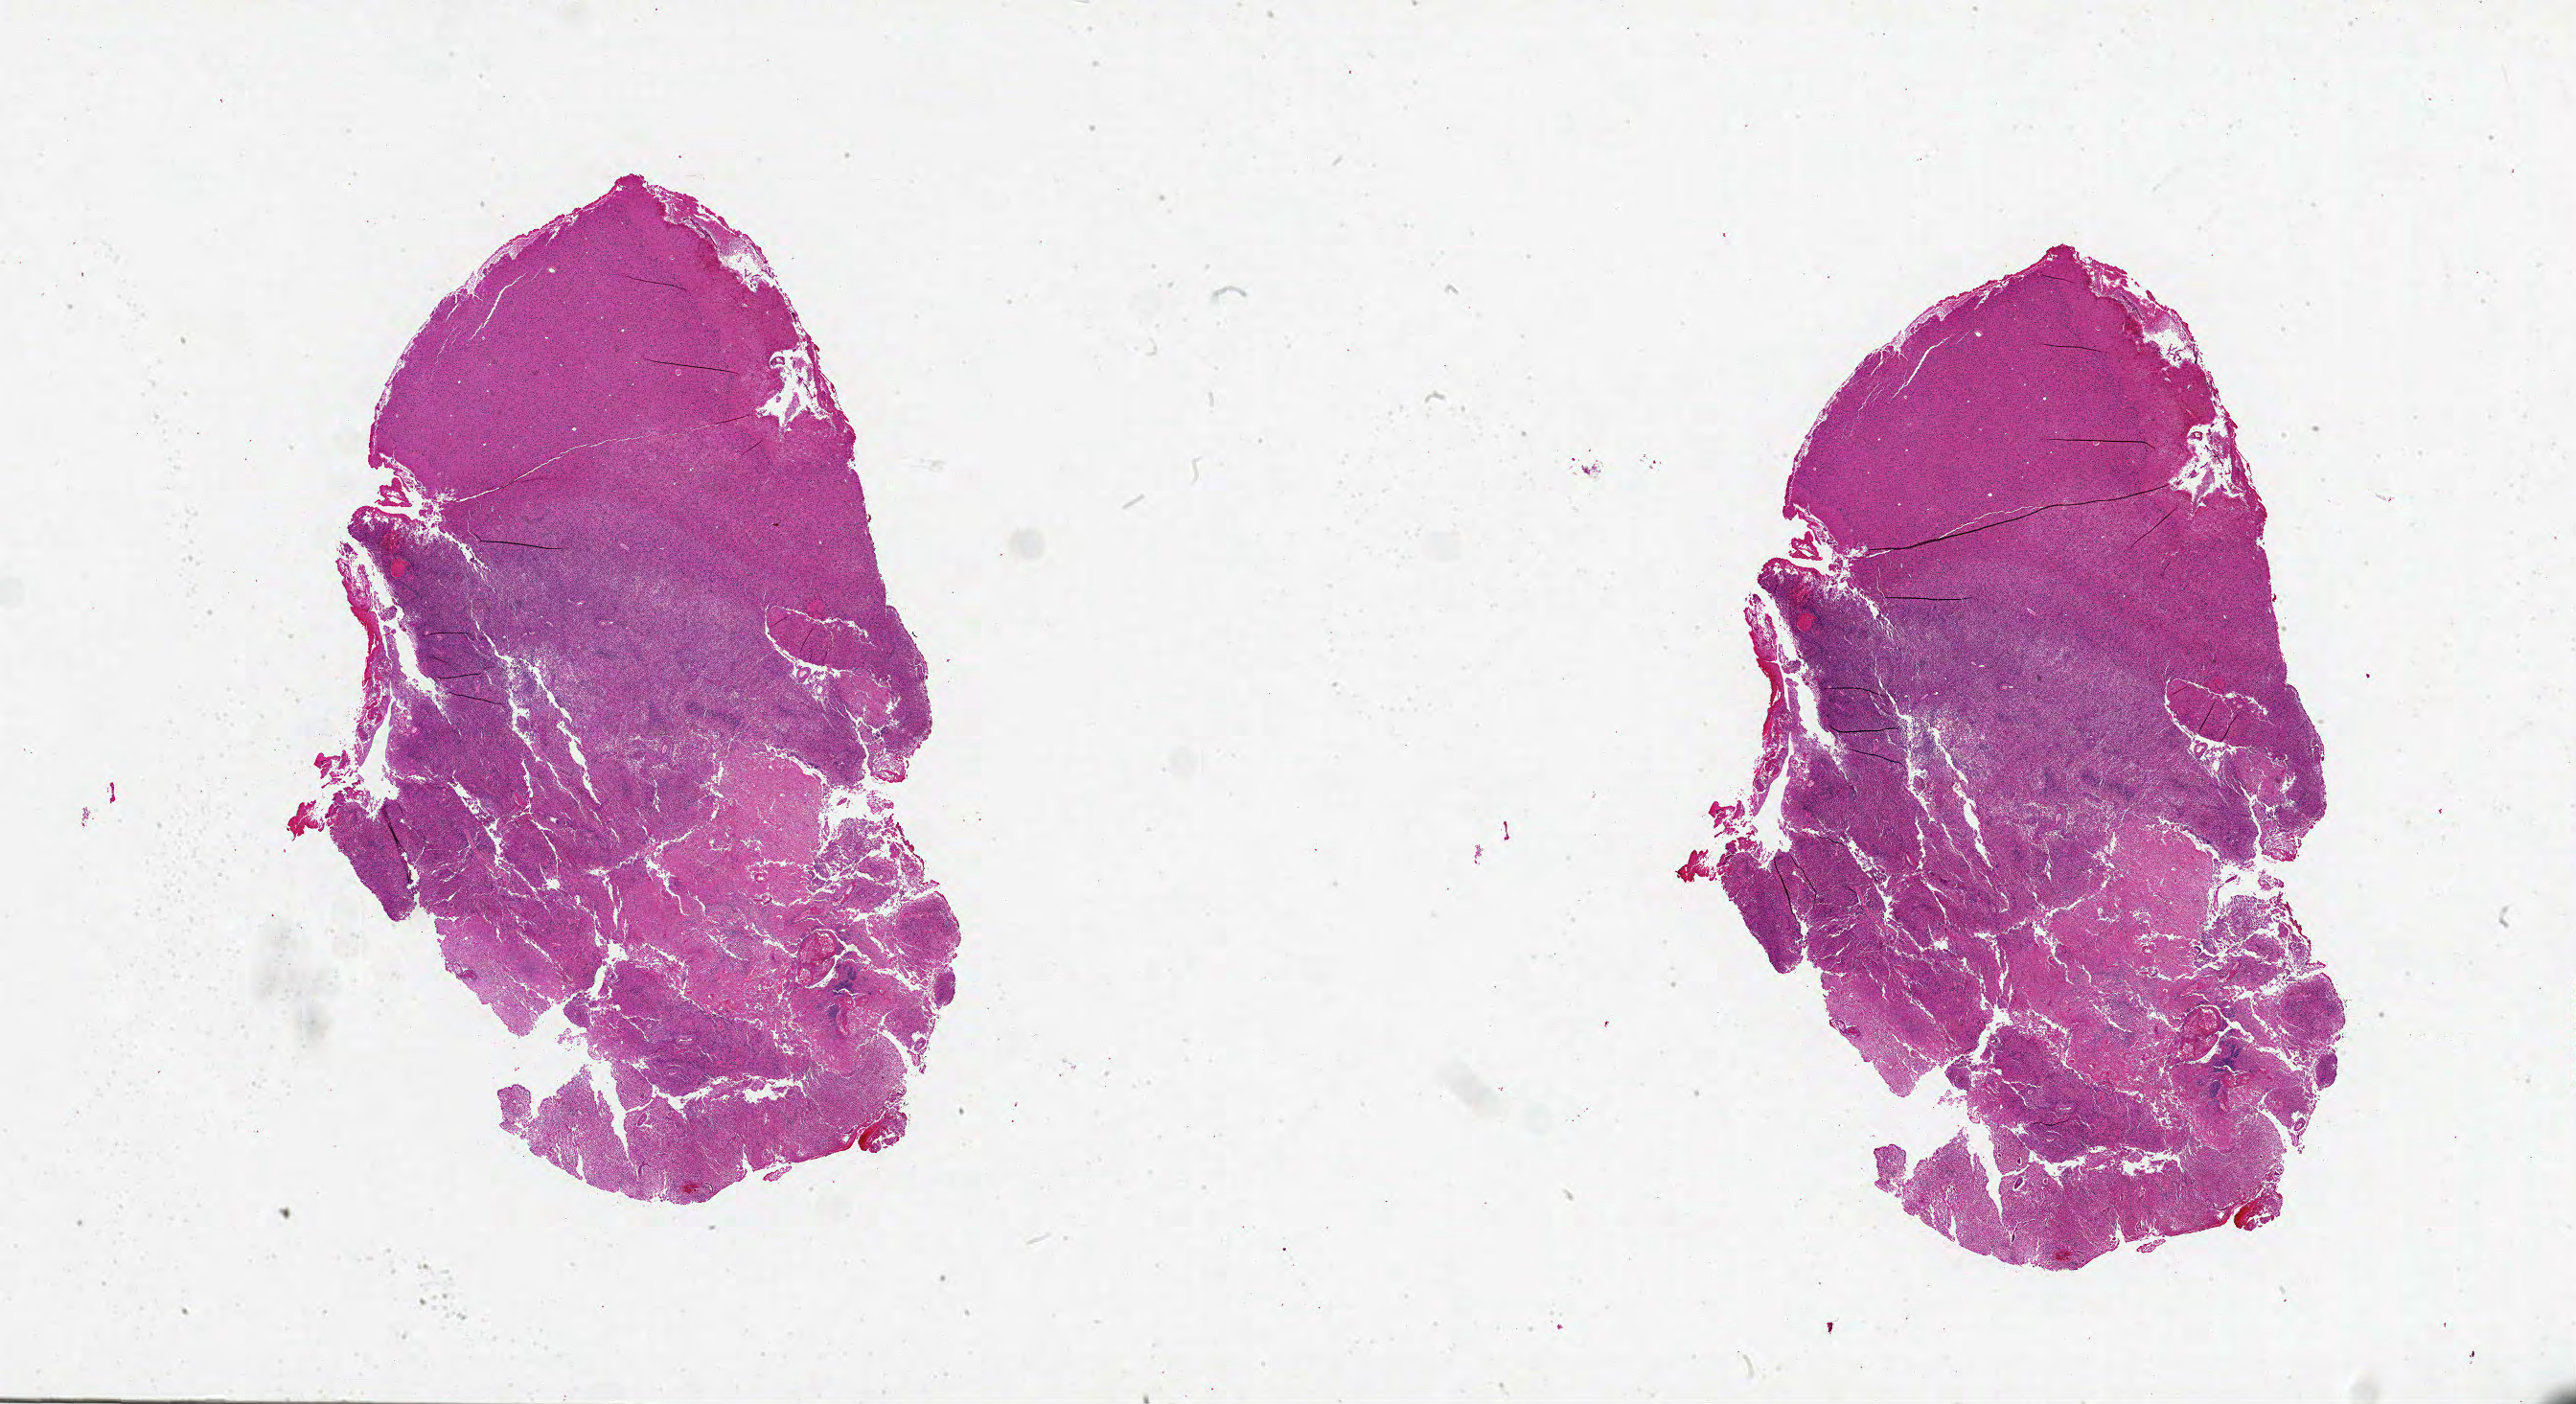
Hematoxylin and eosin (H&E) stained whole-slide image — shown as a low-resolution overview of the whole scanned area (about 43.0 x 23.4 mm, slide scanned at 20x); formalin-fixed paraffin-embedded (FFPE) diagnostic section; sample: primary tumour, brain. Patient: male, age at initial diagnosis 77 years.
Diagnosis: Glioblastoma.